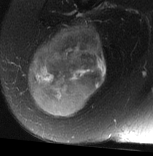
MRI of an extremity soft-tissue mass, one axial slice; position 30 of 77 along the scan axis; T2-weighted fat-saturated; MR volume resampled by the dataset authors to the PET/CT grid (not the native acquisition matrix); 3.27 mm slice thickness; 153 × 156 image matrix. Female patient. From the clinical record (not read from this slice): histological type: synovial sarcoma; grade: intermediate; site of the primary tumour: right buttock.
Outlined on this slice (expert contour drawn on MRI and transferred to this co-registered scan by the dataset authors):
- gross tumour volume including surrounding oedema: bounding box [x1, y1, x2, y2] px = [28, 20, 107, 117]
- gross tumour volume (mass): [28, 27, 107, 117]